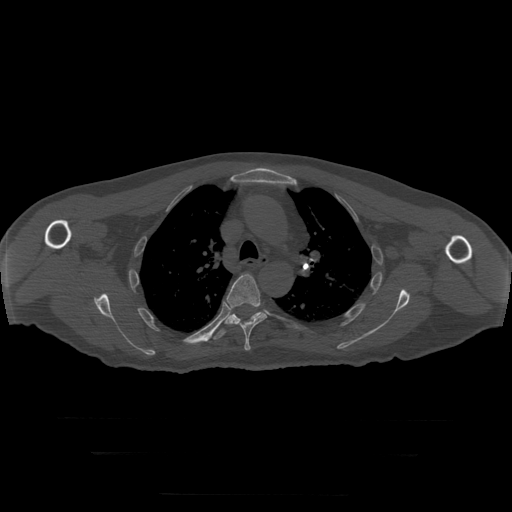
CT including the spine, one axial slice. Position 220 of 397 along the scan axis. Reconstruction kernel STANDARD. 120 kVp. Bone window (W 1800 / L 400 HU). 1.25 mm slice thickness. 512 × 512 image matrix, field of view 510 × 510 mm. Patient age 73 years. Case-level facts recorded for this patient, not image findings: primary cancer: prostate.
Outlined on this slice (semi-automatically segmented with operator editing):
- T5 vertebra: bounding box [x1, y1, x2, y2] px = [225, 275, 267, 351]
- T6 vertebra: [210, 312, 263, 340]